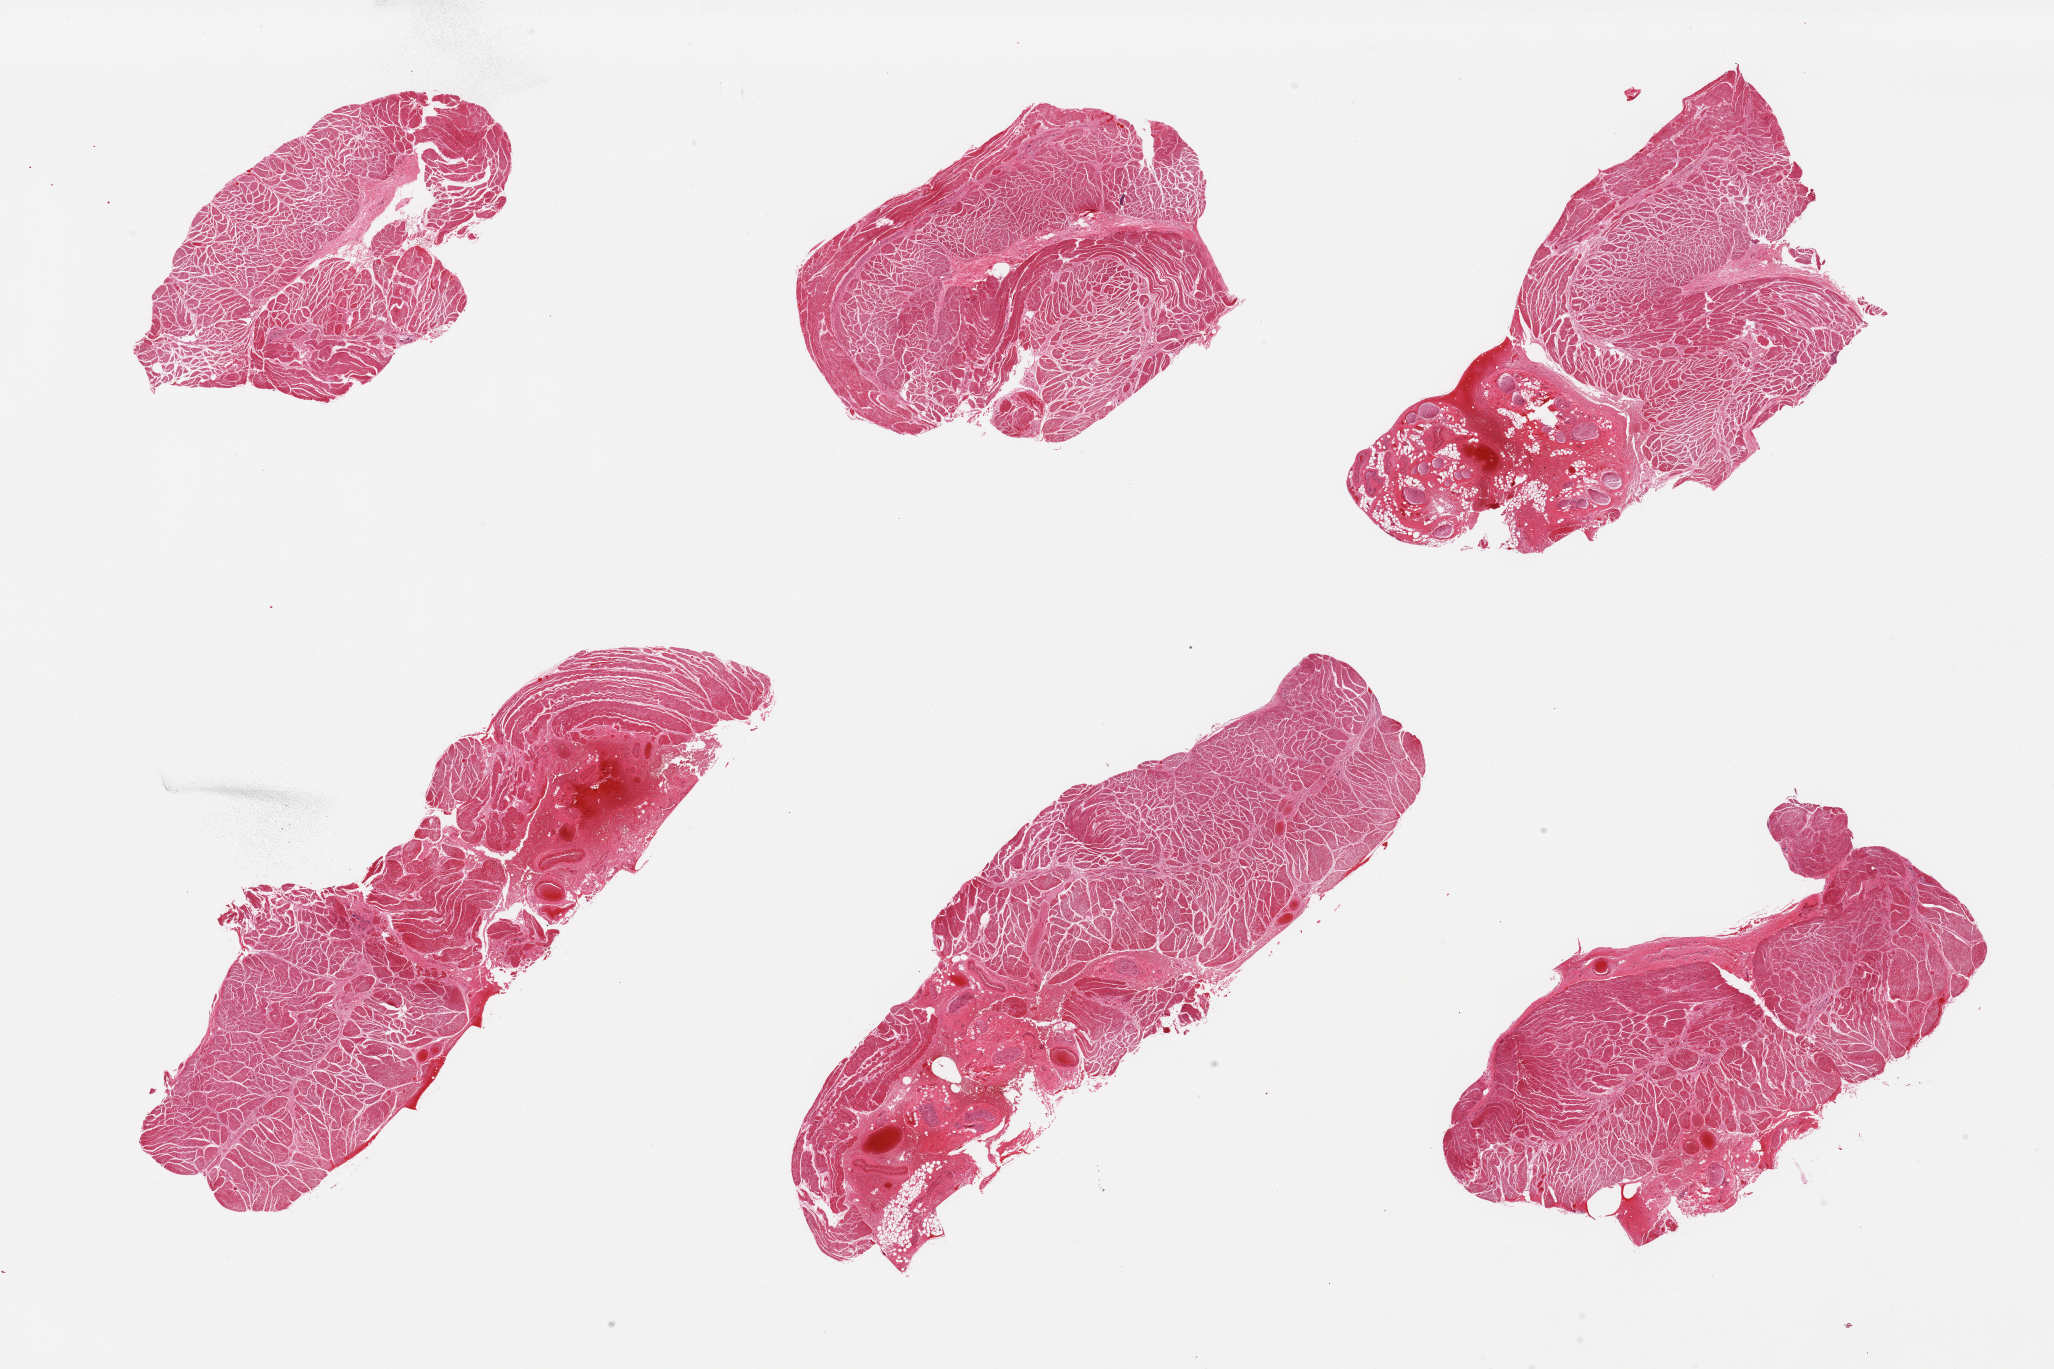
Whole-slide image, H&E stain — shown as a low-resolution overview of the whole scanned area (about 32.5 x 21.7 mm, slide scanned at 20x); PAXgene-fixed, paraffin-embedded tissue; section of esophageal muscle (target tissue); donor tissue sample. Male donor.
Review note (as recorded): 6 pieces, 2 pieces include ~30% fat, vessels, and nerve.